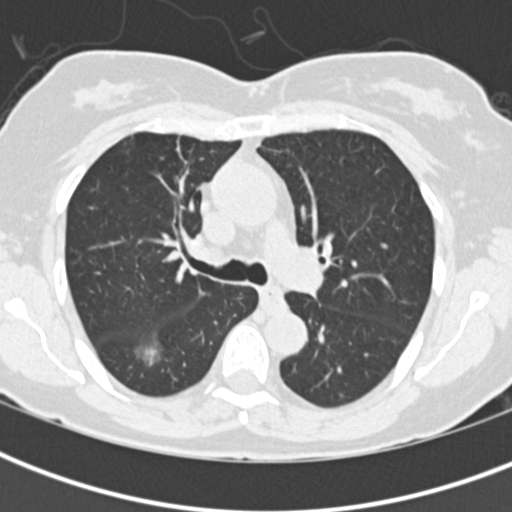
Low-dose screening chest CT, one axial slice; reconstruction kernel B30f; lung window (W 1500 / L -600 HU); 512 × 512 image matrix, field of view 290 × 290 mm.
Structures marked on this image (manually delineated by an expert):
- lesion 1 (tumor, lower lobe of right lung): bounding box [x1, y1, x2, y2] px = [142, 346, 161, 365]